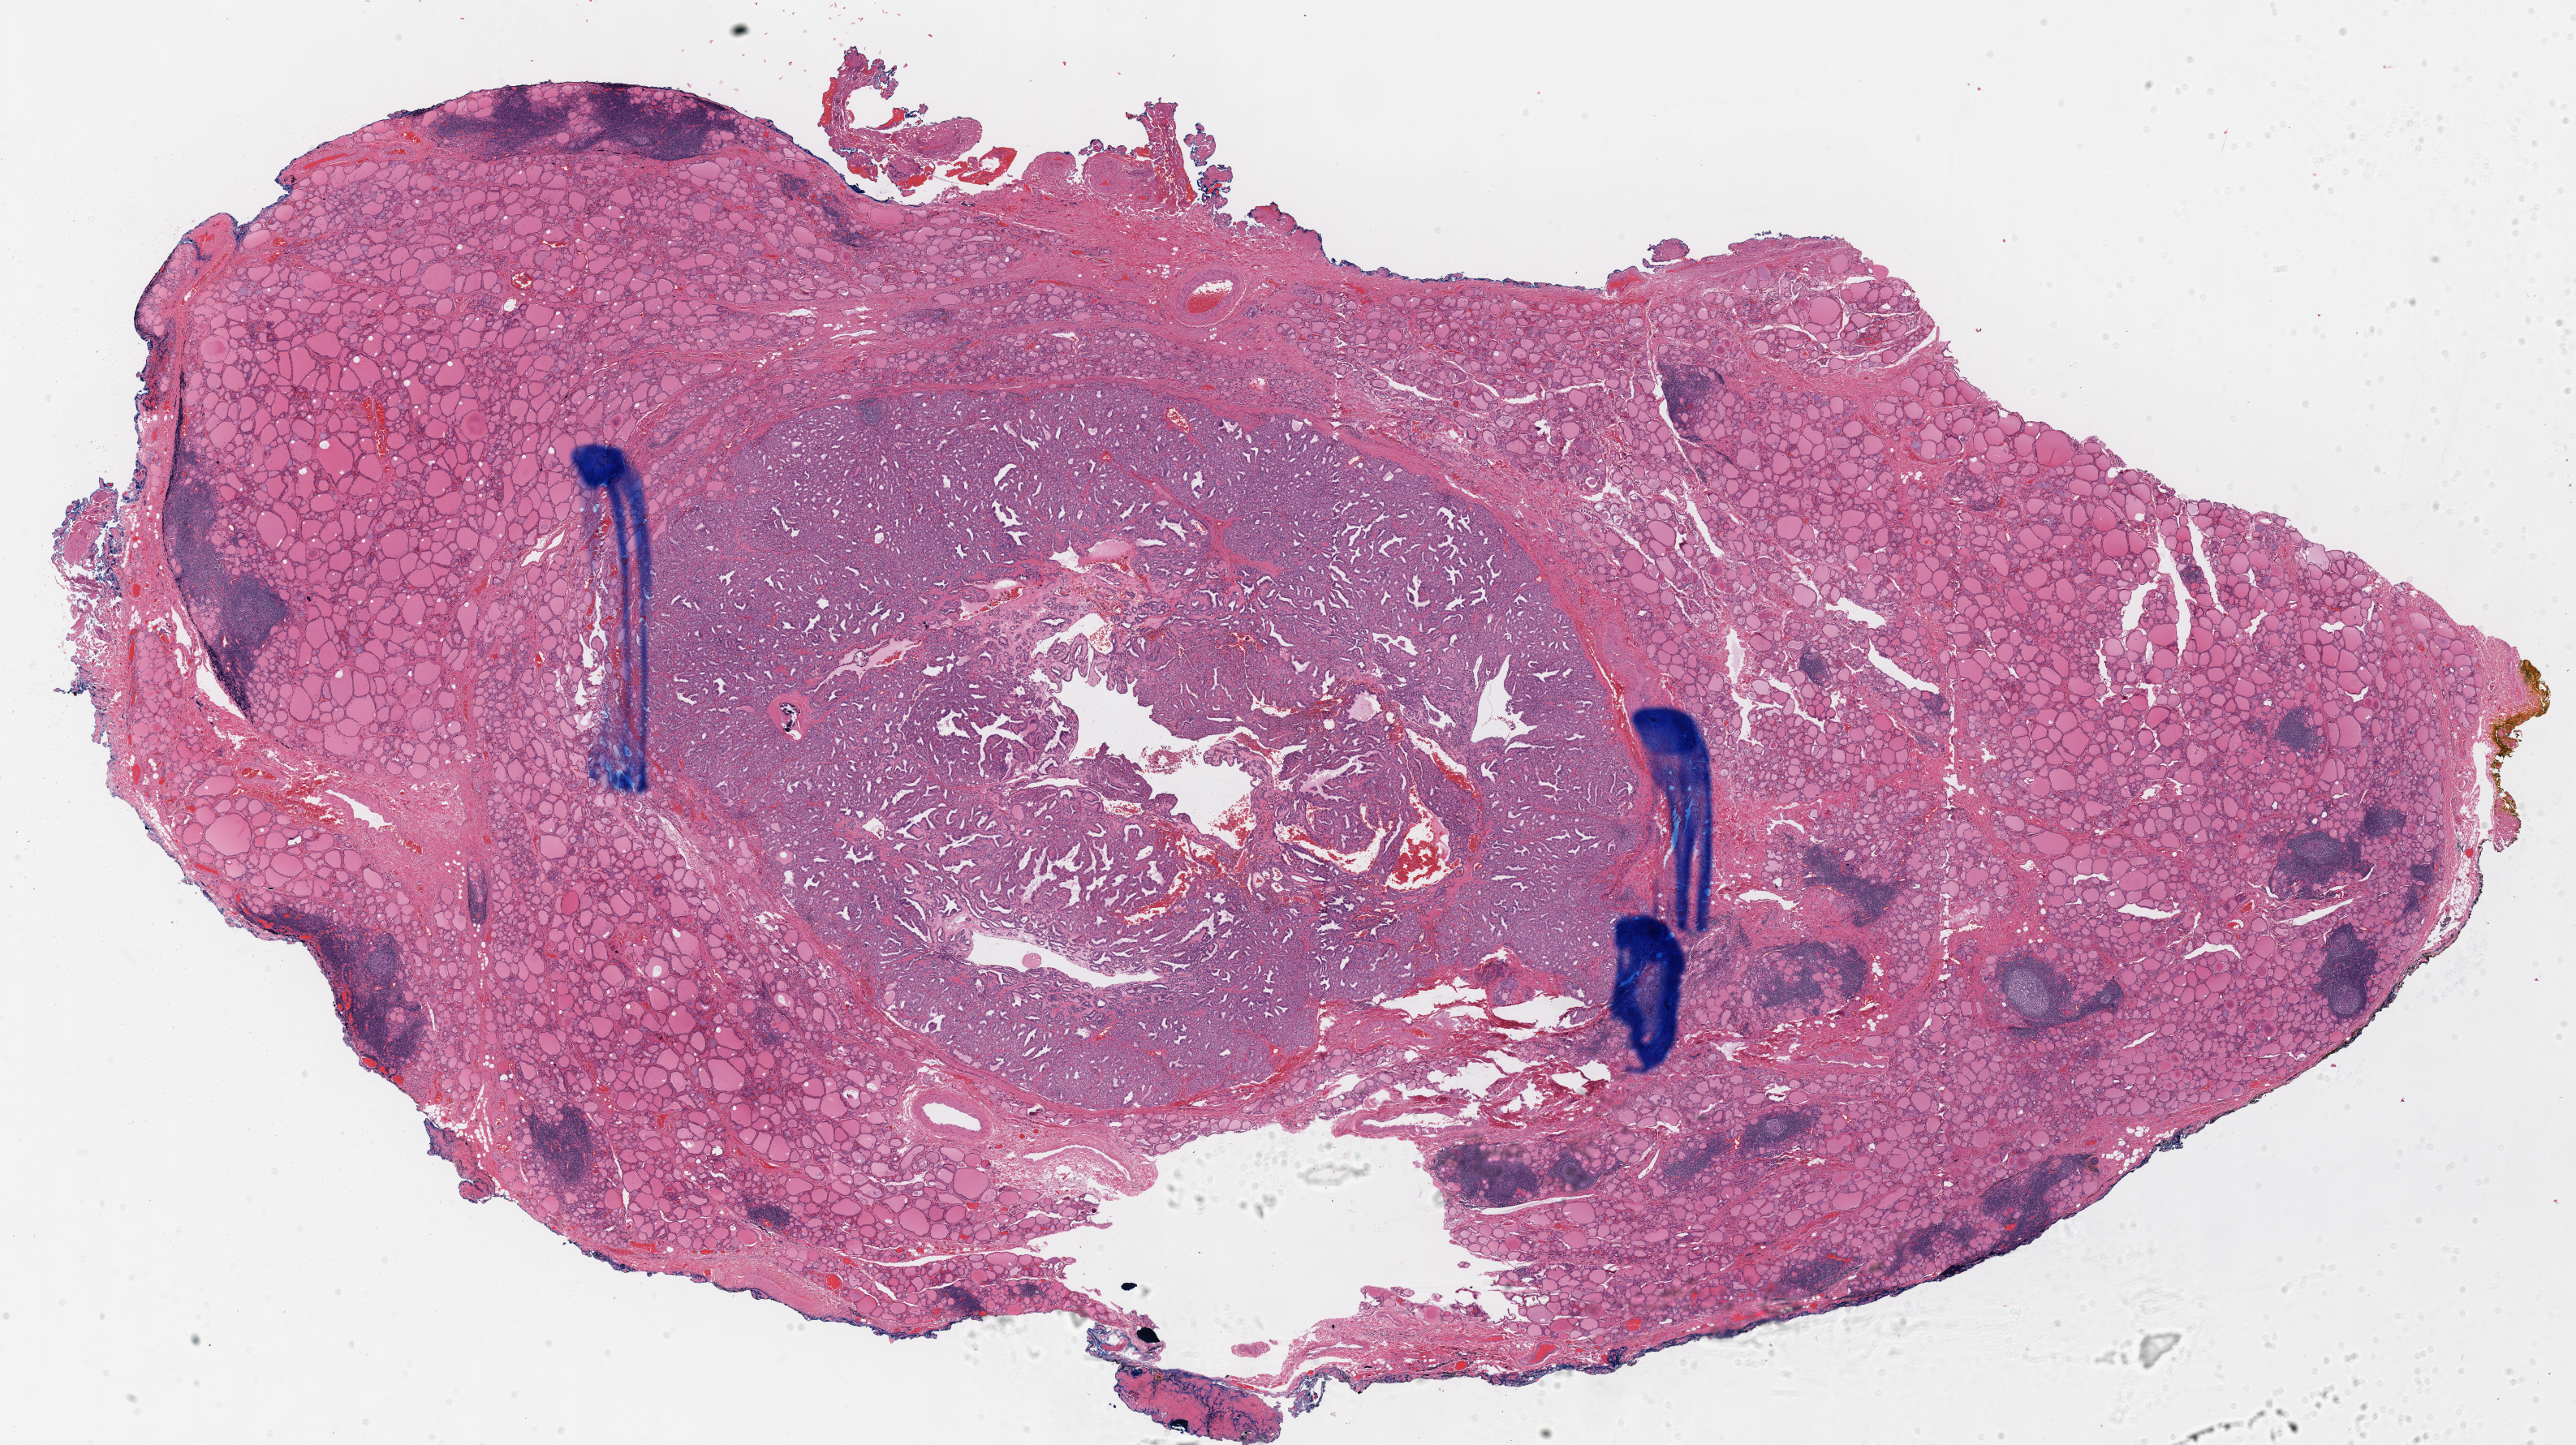
H&E-stained whole-slide image, whole scanned area (about 25.0 x 14.0 mm) shown as a low-resolution overview, formalin-fixed paraffin-embedded (FFPE) diagnostic section, primary tumour sample from the thyroid. Patient: female, age at initial diagnosis 48 years.
Pathologic diagnosis: Papillary adenocarcinoma, NOS (thyroid gland). Lymph nodes positive (case pathology): 0 of 6 examined. AJCC pathologic stage: III (7th edition).